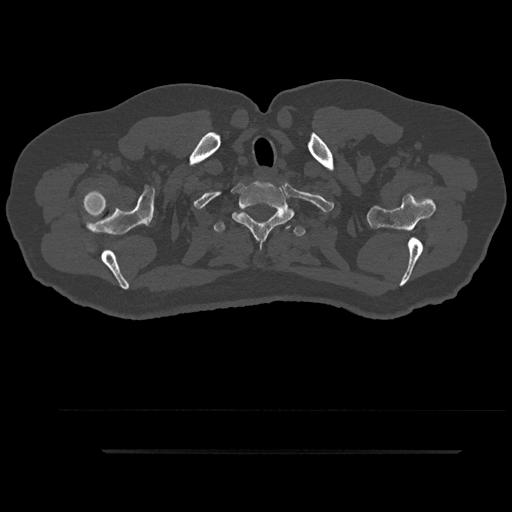
CT including the spine, one axial slice; 120 kVp; bone window (W 1800 / L 400 HU); 512 × 512 image matrix, field of view 432 × 432 mm. Patient: male, 63 years. Case-level facts recorded for this patient, not image findings: primary cancer: renal.
Structures marked on this image (semi-automatically segmented with operator editing):
- T1 vertebra: bounding box [x1, y1, x2, y2] px = [232, 185, 296, 248]
- T2 vertebra: [214, 222, 306, 237]